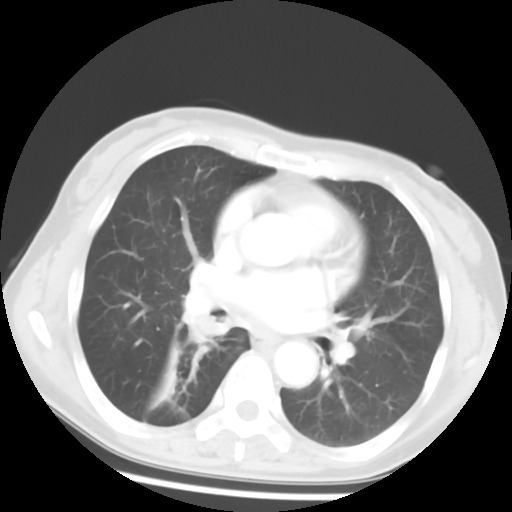
Chest CT, one axial slice; slice 28 of 52 in the series (ordered by position); 120 kVp; lung window (W 1500 / L -600 HU); 5 mm slice thickness; 512 × 512 image matrix. Patient: female, 54 years. Case-level facts recorded for this patient, not image findings: clinical TNM (as recorded): T1c N0 M0; histopathological grade: G1-2.
Structures marked on this image (bounding box drawn by a radiologist):
- lung tumour (recorded histology: squamous cell carcinoma): bounding box <181,296,237,353> (left, top, right, bottom; pixels)